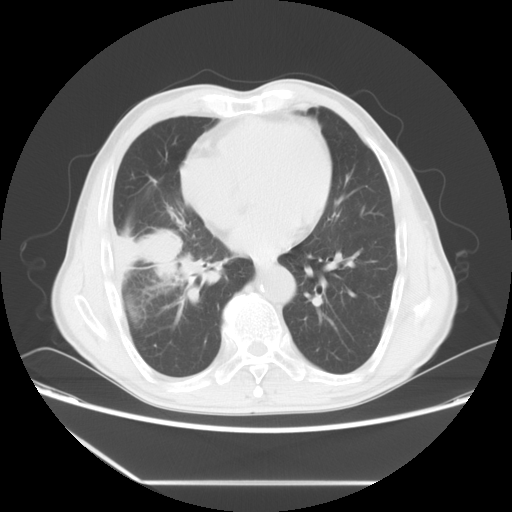
Chest CT, one axial slice; slice 25 of 60 in the series (ordered by position); reconstruction kernel STANDARD; 120 kVp; lung window (W 1500 / L -600 HU); 512 × 512 image matrix, field of view 386 × 386 mm. Male patient, age 72 years. From the clinical record (not read from this slice): clinical TNM (as recorded): T1c N0 M0.
Structures marked on this image (rectangle marked by the reading radiologist):
- lung tumour (recorded histology: squamous cell carcinoma): bounding box <113,213,187,289> (left, top, right, bottom; pixels)